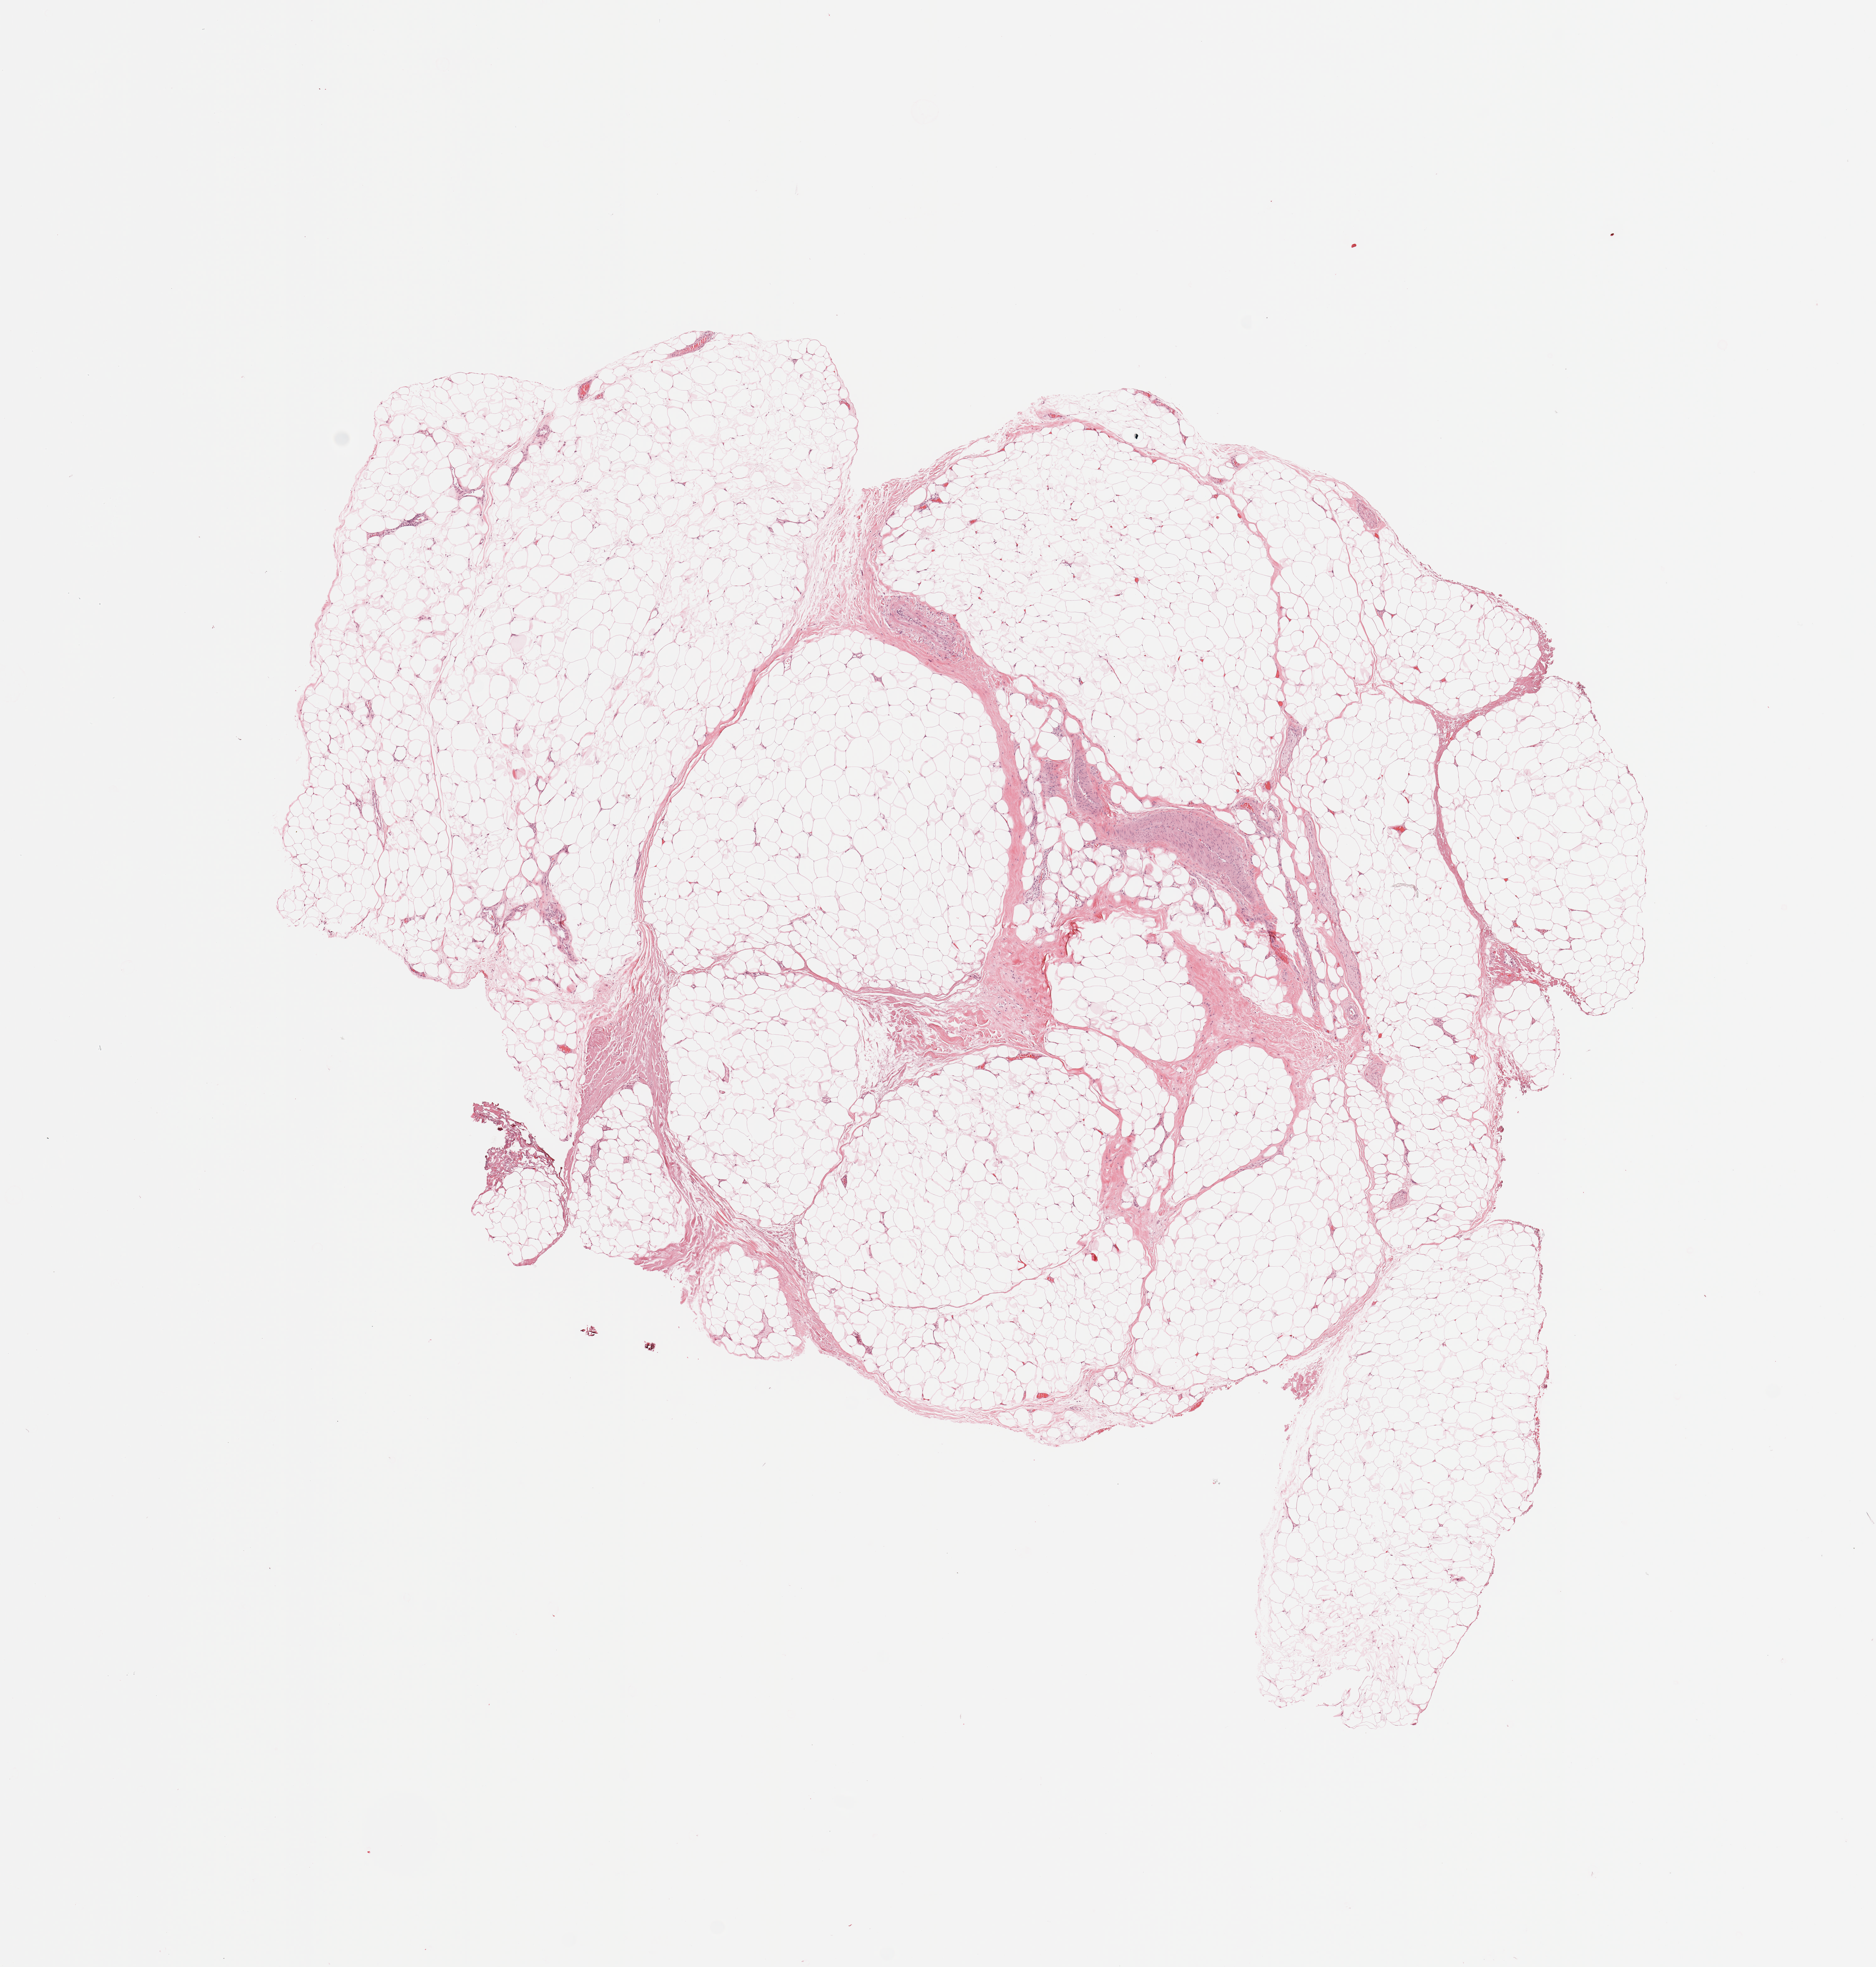
H&E-stained whole-slide image — whole scanned area (about 11.8 x 12.4 mm, acquisition: 20x scan) shown as a low-resolution overview, normal (non-tumour) tissue sample. Patient: male, age 52 years.
This section: normal (non-tumour) tissue from the same patient. Patient diagnosis (cohort enrolment): sarcoma (site not recorded at cohort level).